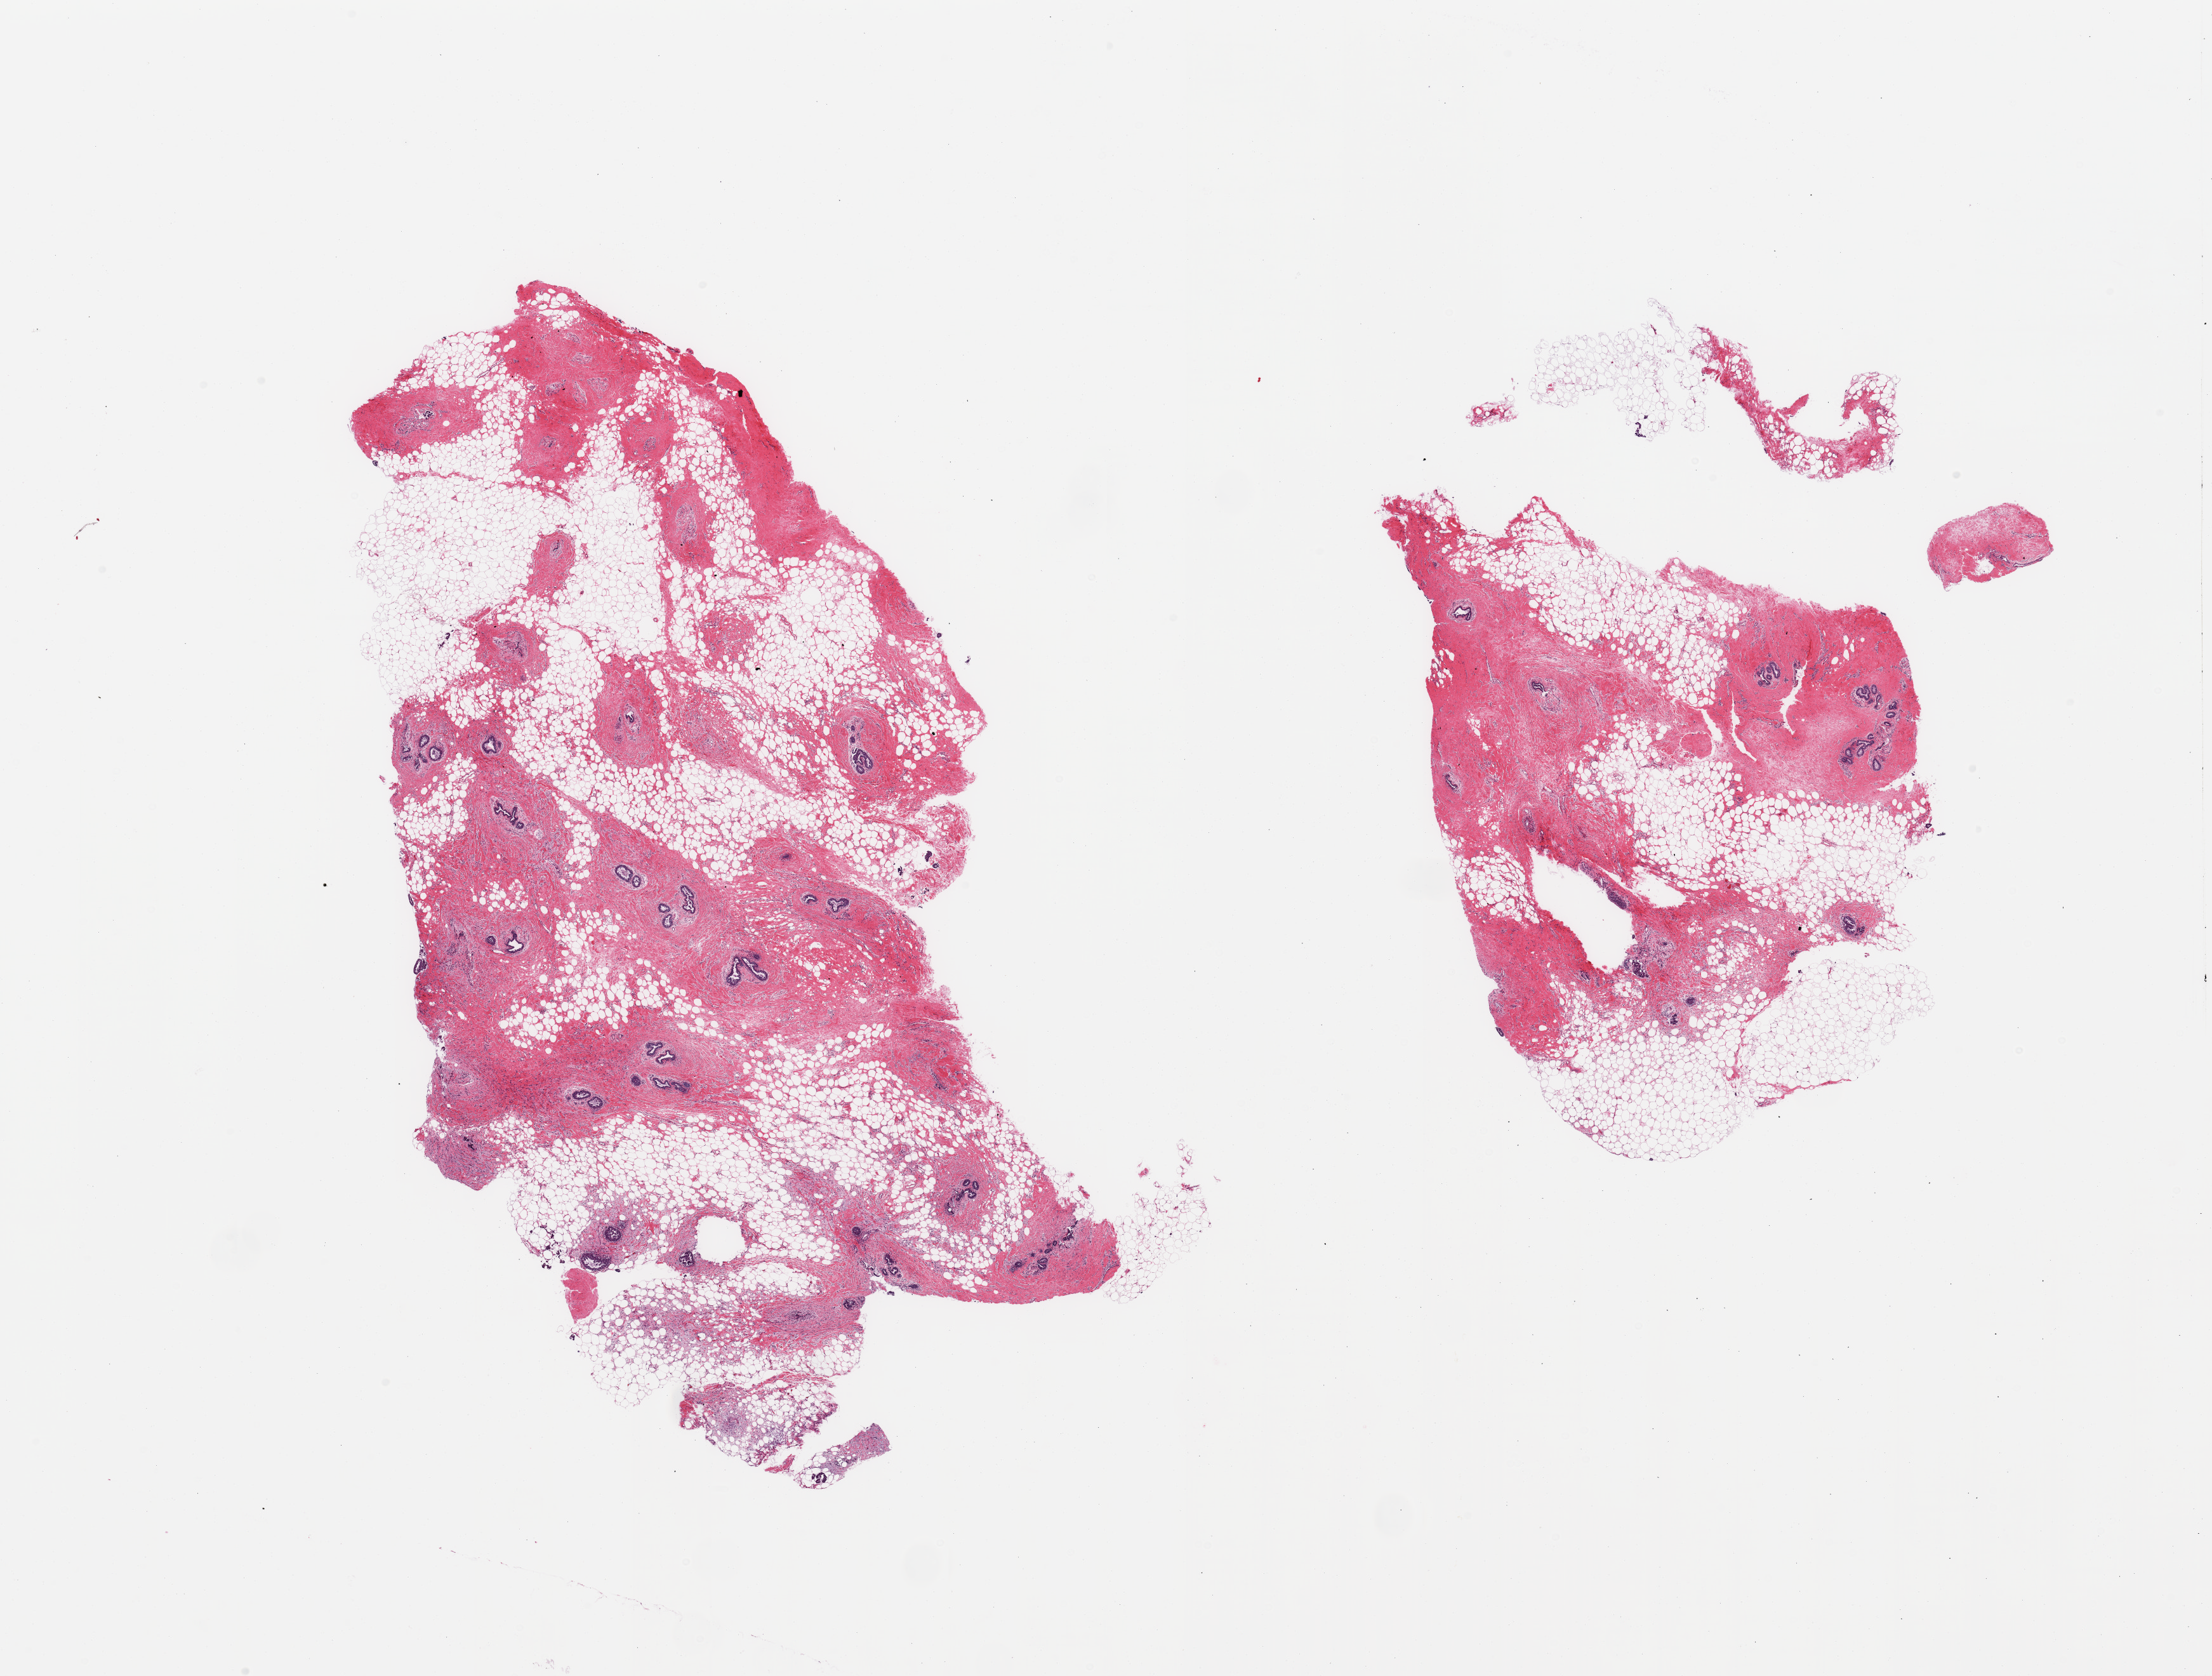
Whole-slide image, H&E stain — low-resolution overview of the scanned area, about 27.6 x 20.9 mm (slide scanned at 20x), PAXgene-fixed paraffin-embedded (PFPE) section, sampled site (target tissue): breast, tissue donor sample.
- pathologist's review note for this sample: 2 pieces; gynecomastoid ductal and stromal hyperplasia; ~50% adipose tissue